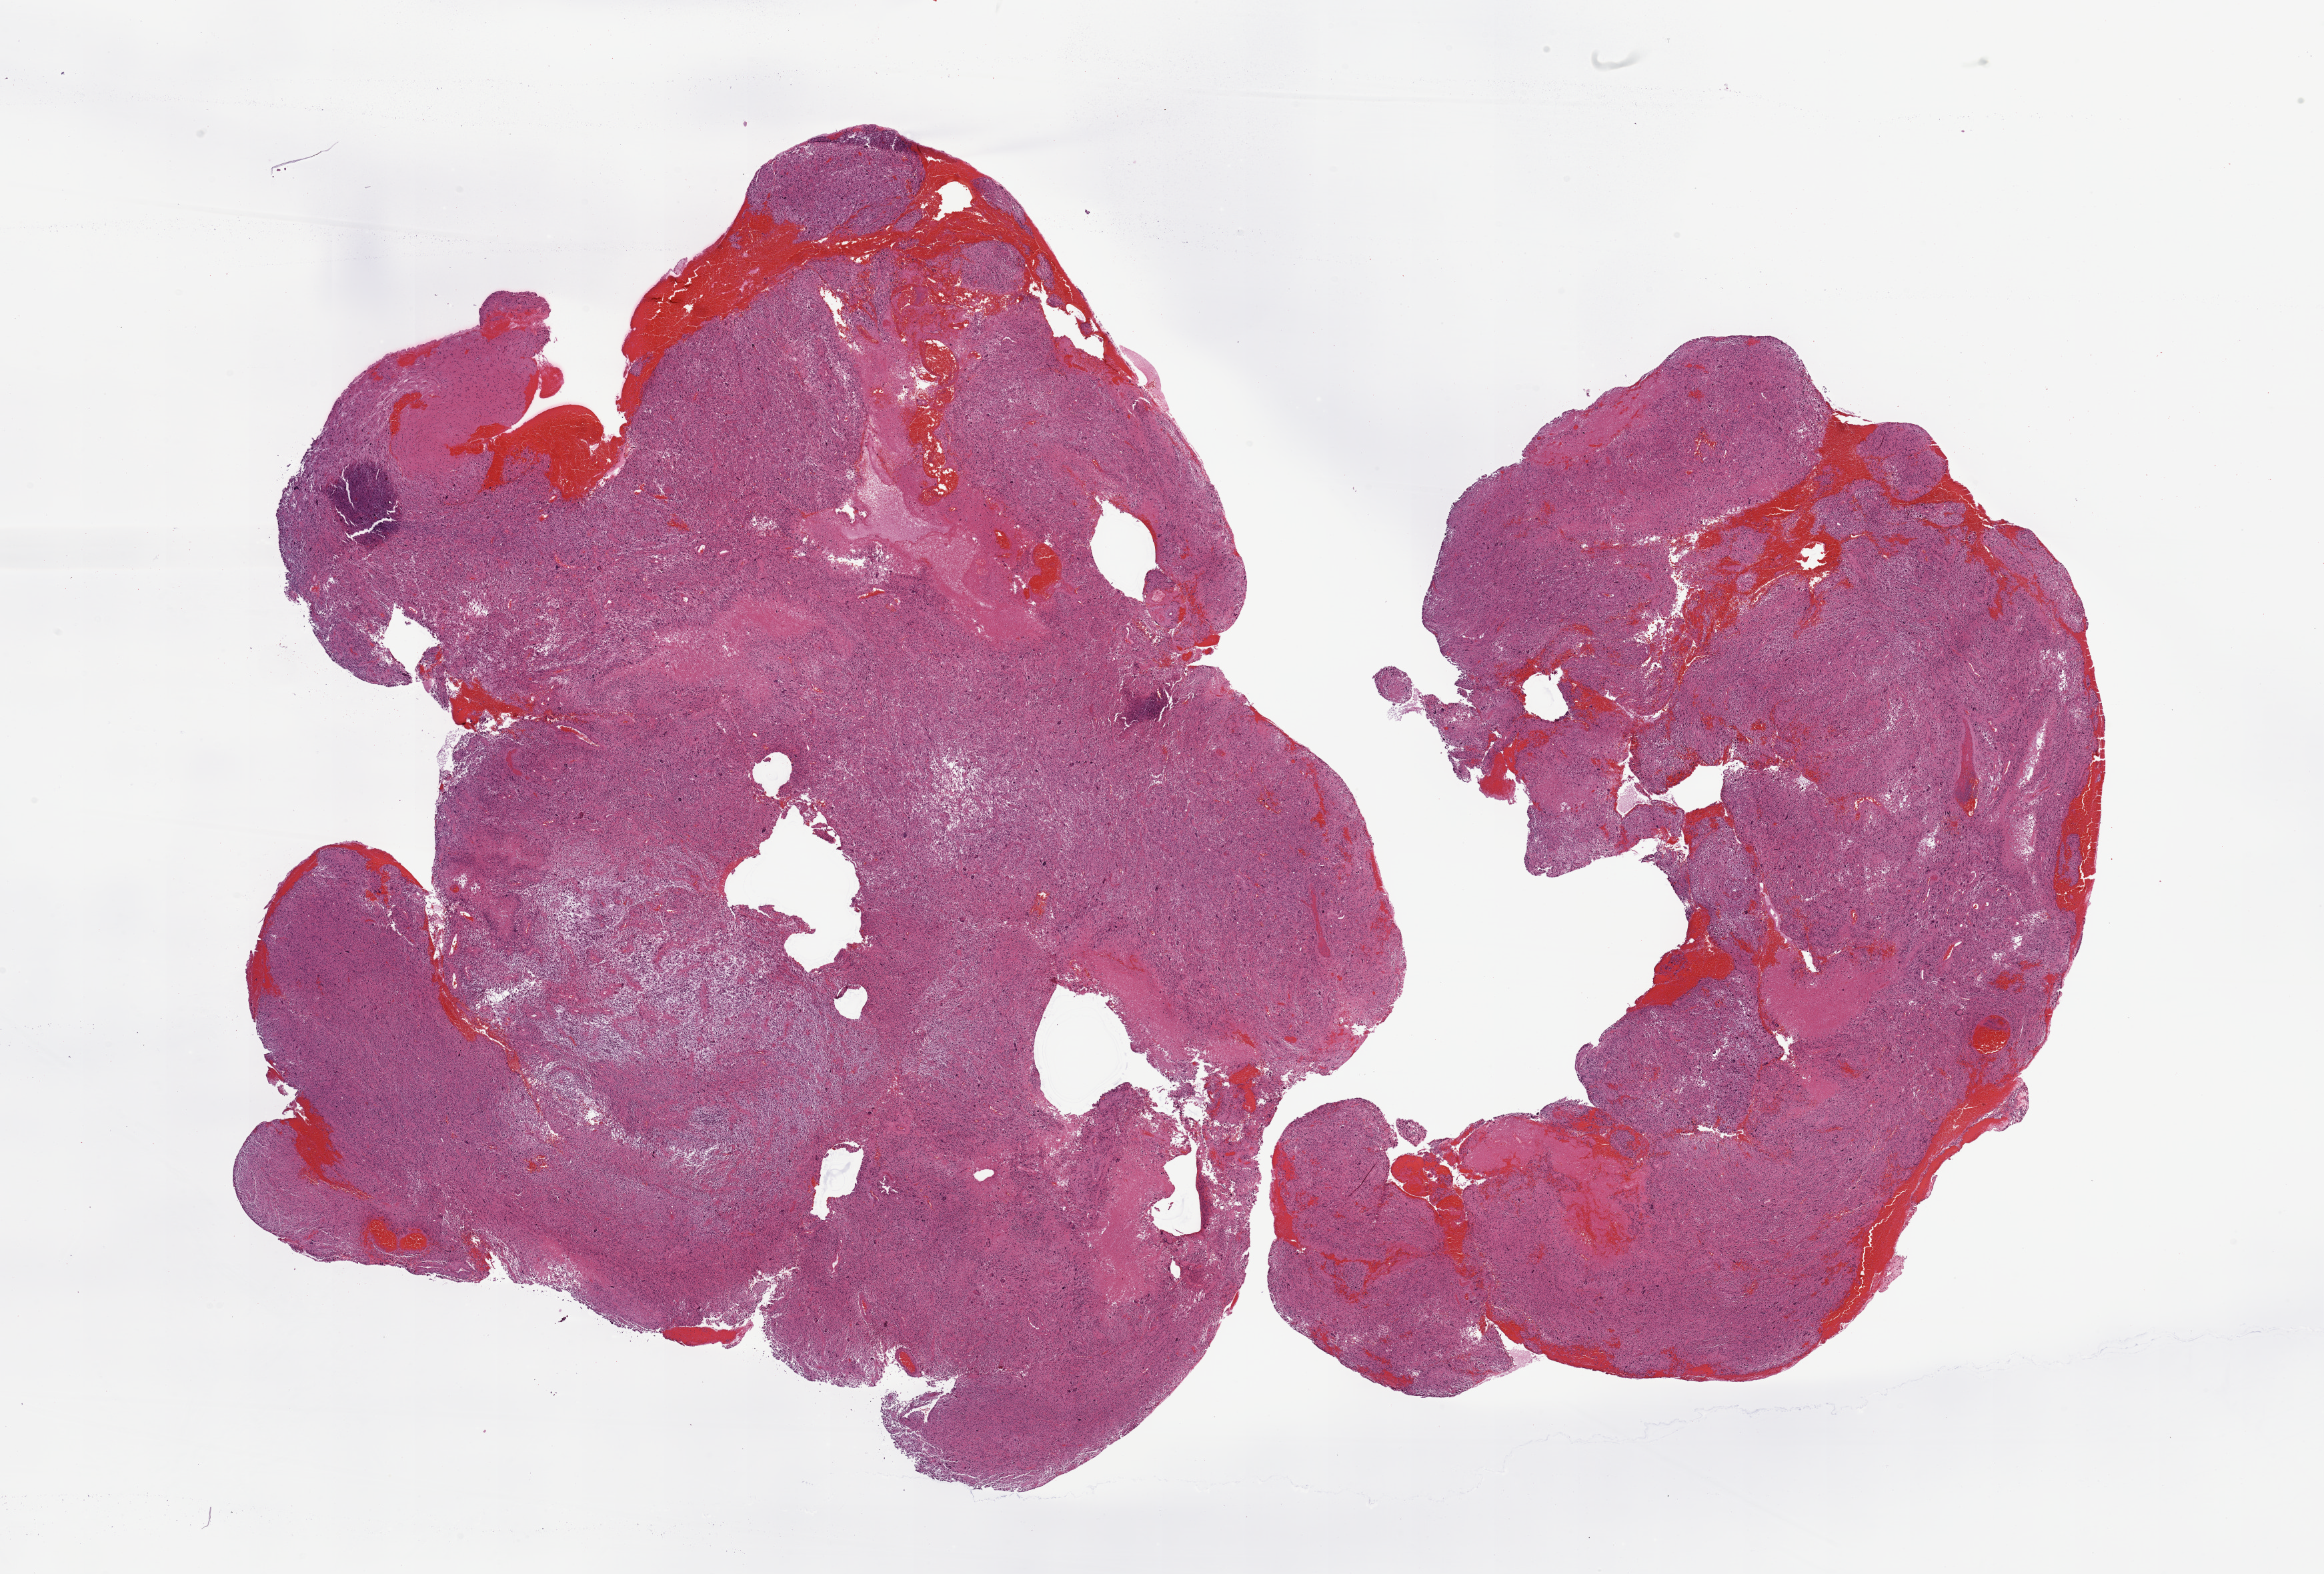
Whole-slide histology image, Hematoxylin and eosin (H&E) stained, low-resolution overview of the scanned area, about 27.6 x 18.7 mm (from a 20x scan); tumour tissue sample, sampled site: brain. Patient: male, age 43 years. Pathologist review of this section (percent, as recorded): tumour nuclei 80%, necrosis 10%.
* primary tumour site (as recorded): parietal lobe
* diagnosis: Glioblastoma